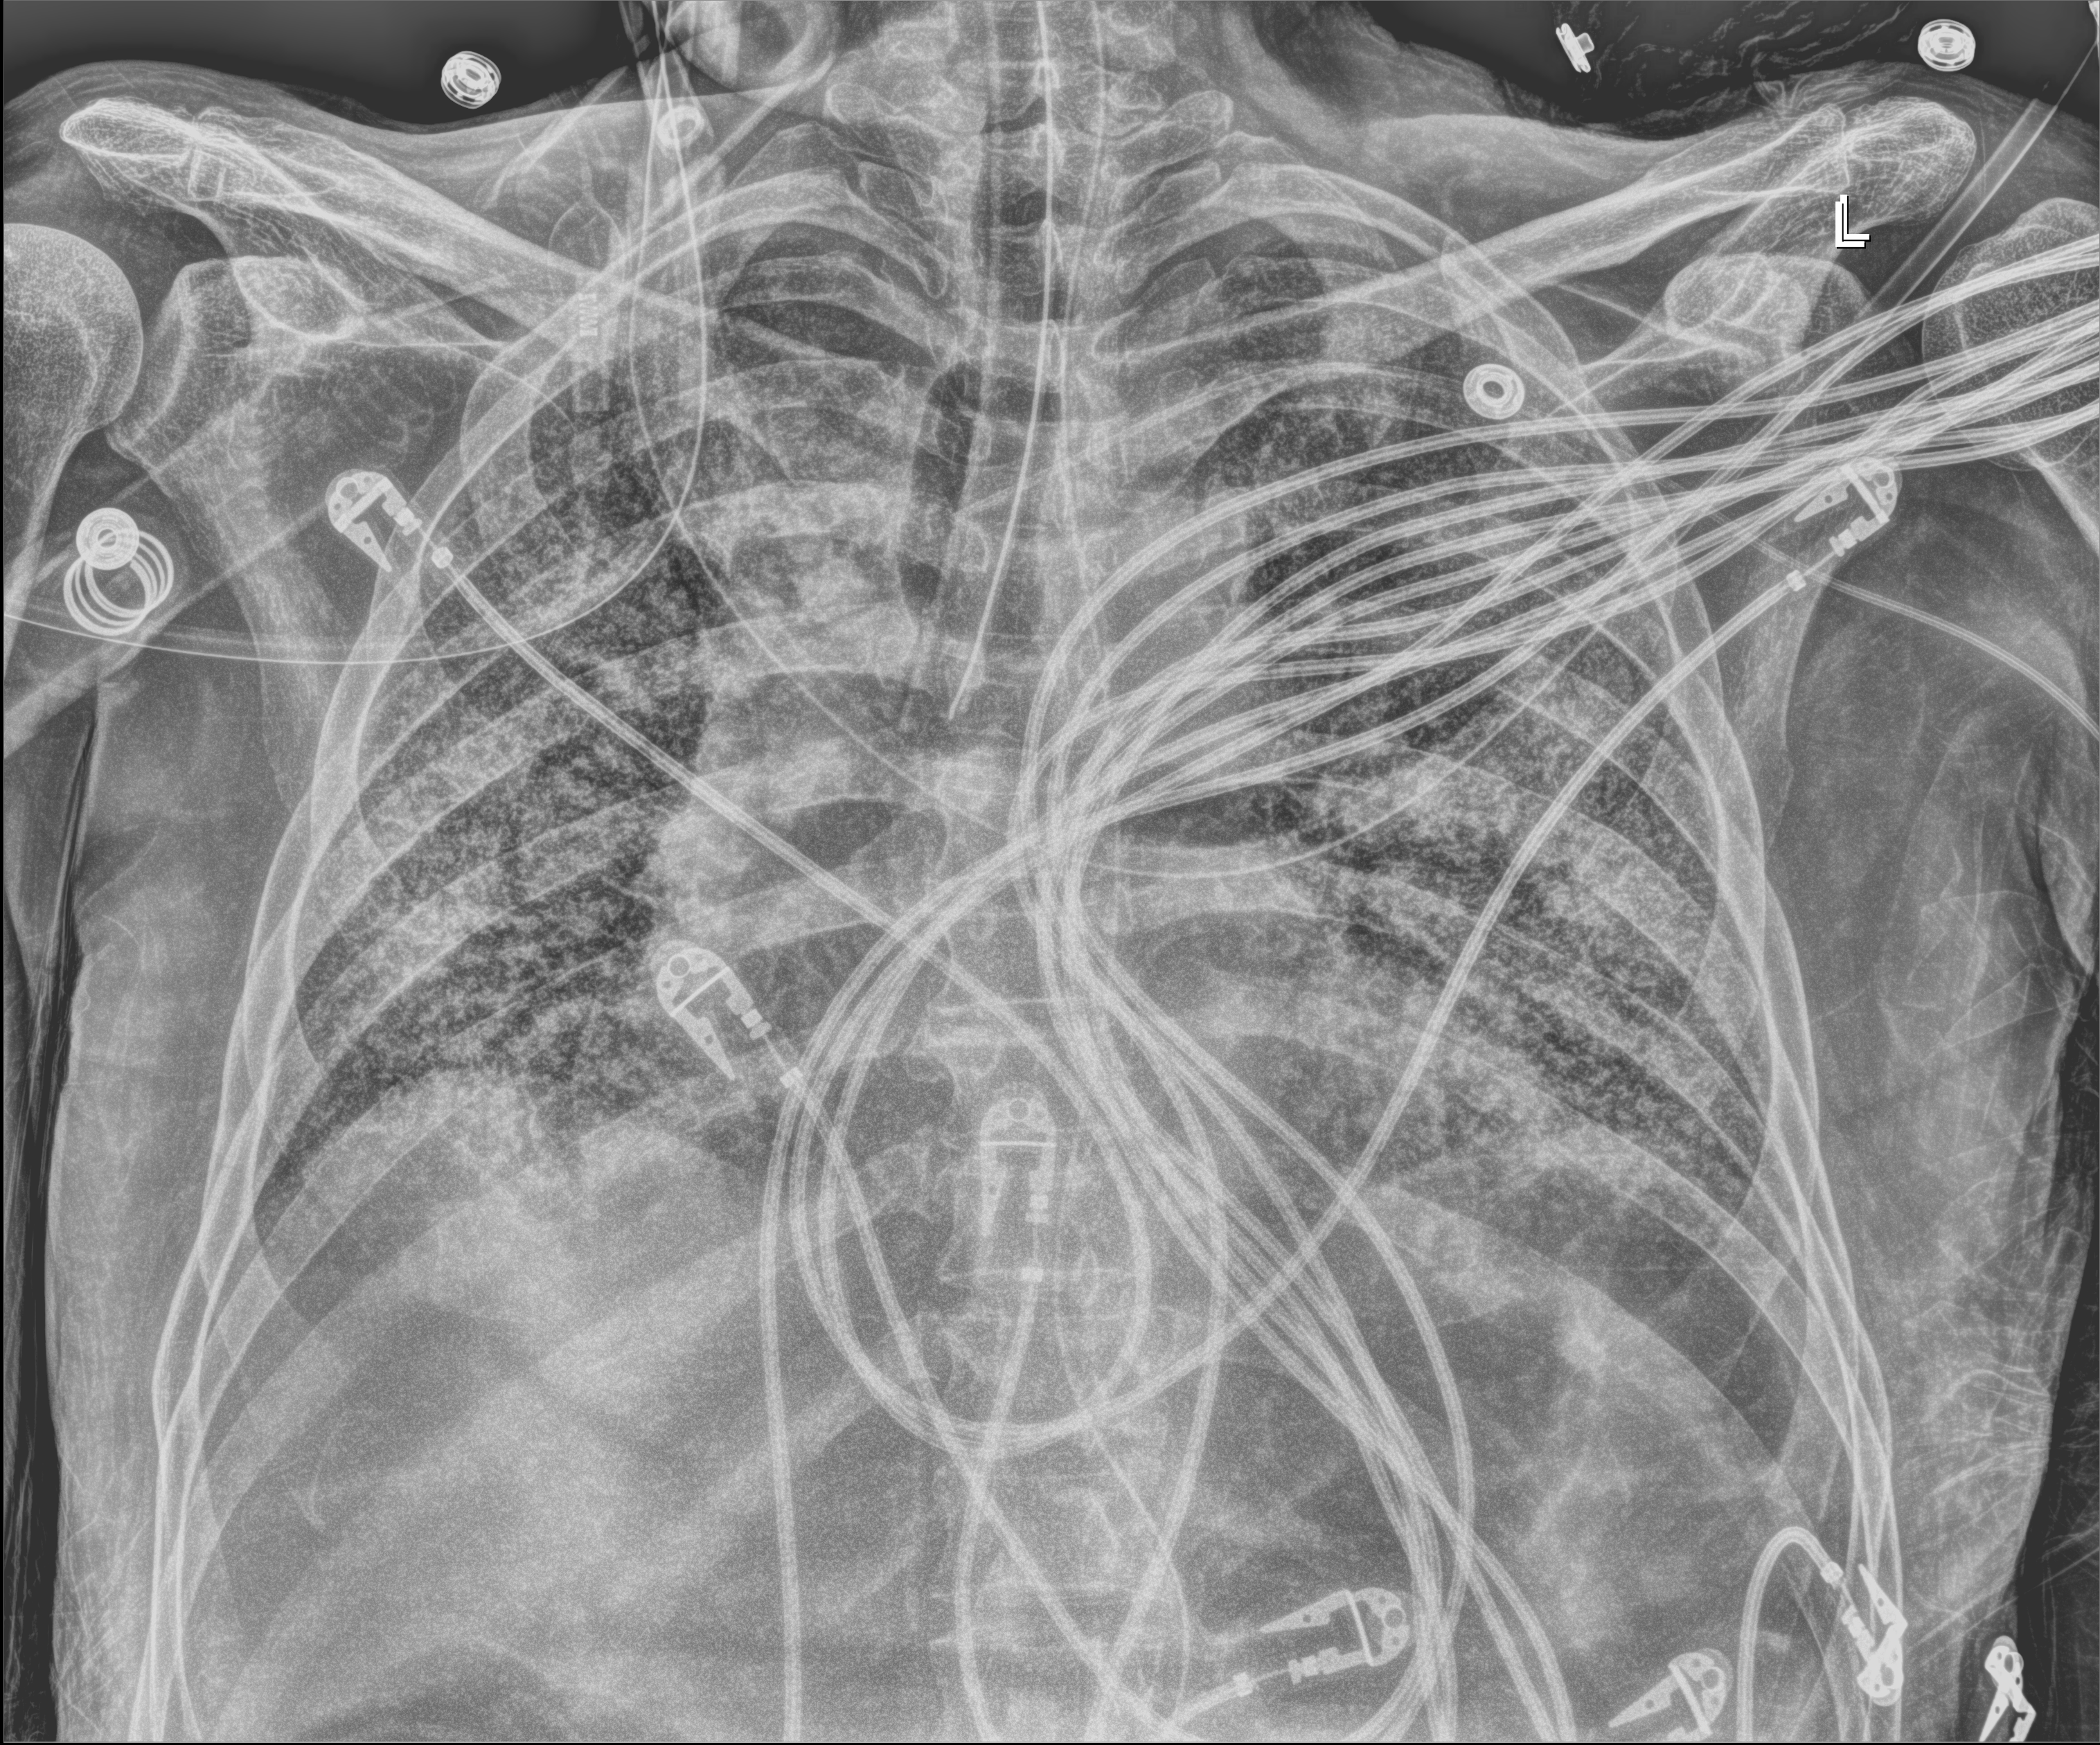
Bedside chest radiograph (digital radiography). Patient hospitalised with COVID-19; male, aged 60–74 years.
Hospital-stay facts (about this admission, not read from this image; timing relative to this image not recorded): length of hospital stay: 54 days.